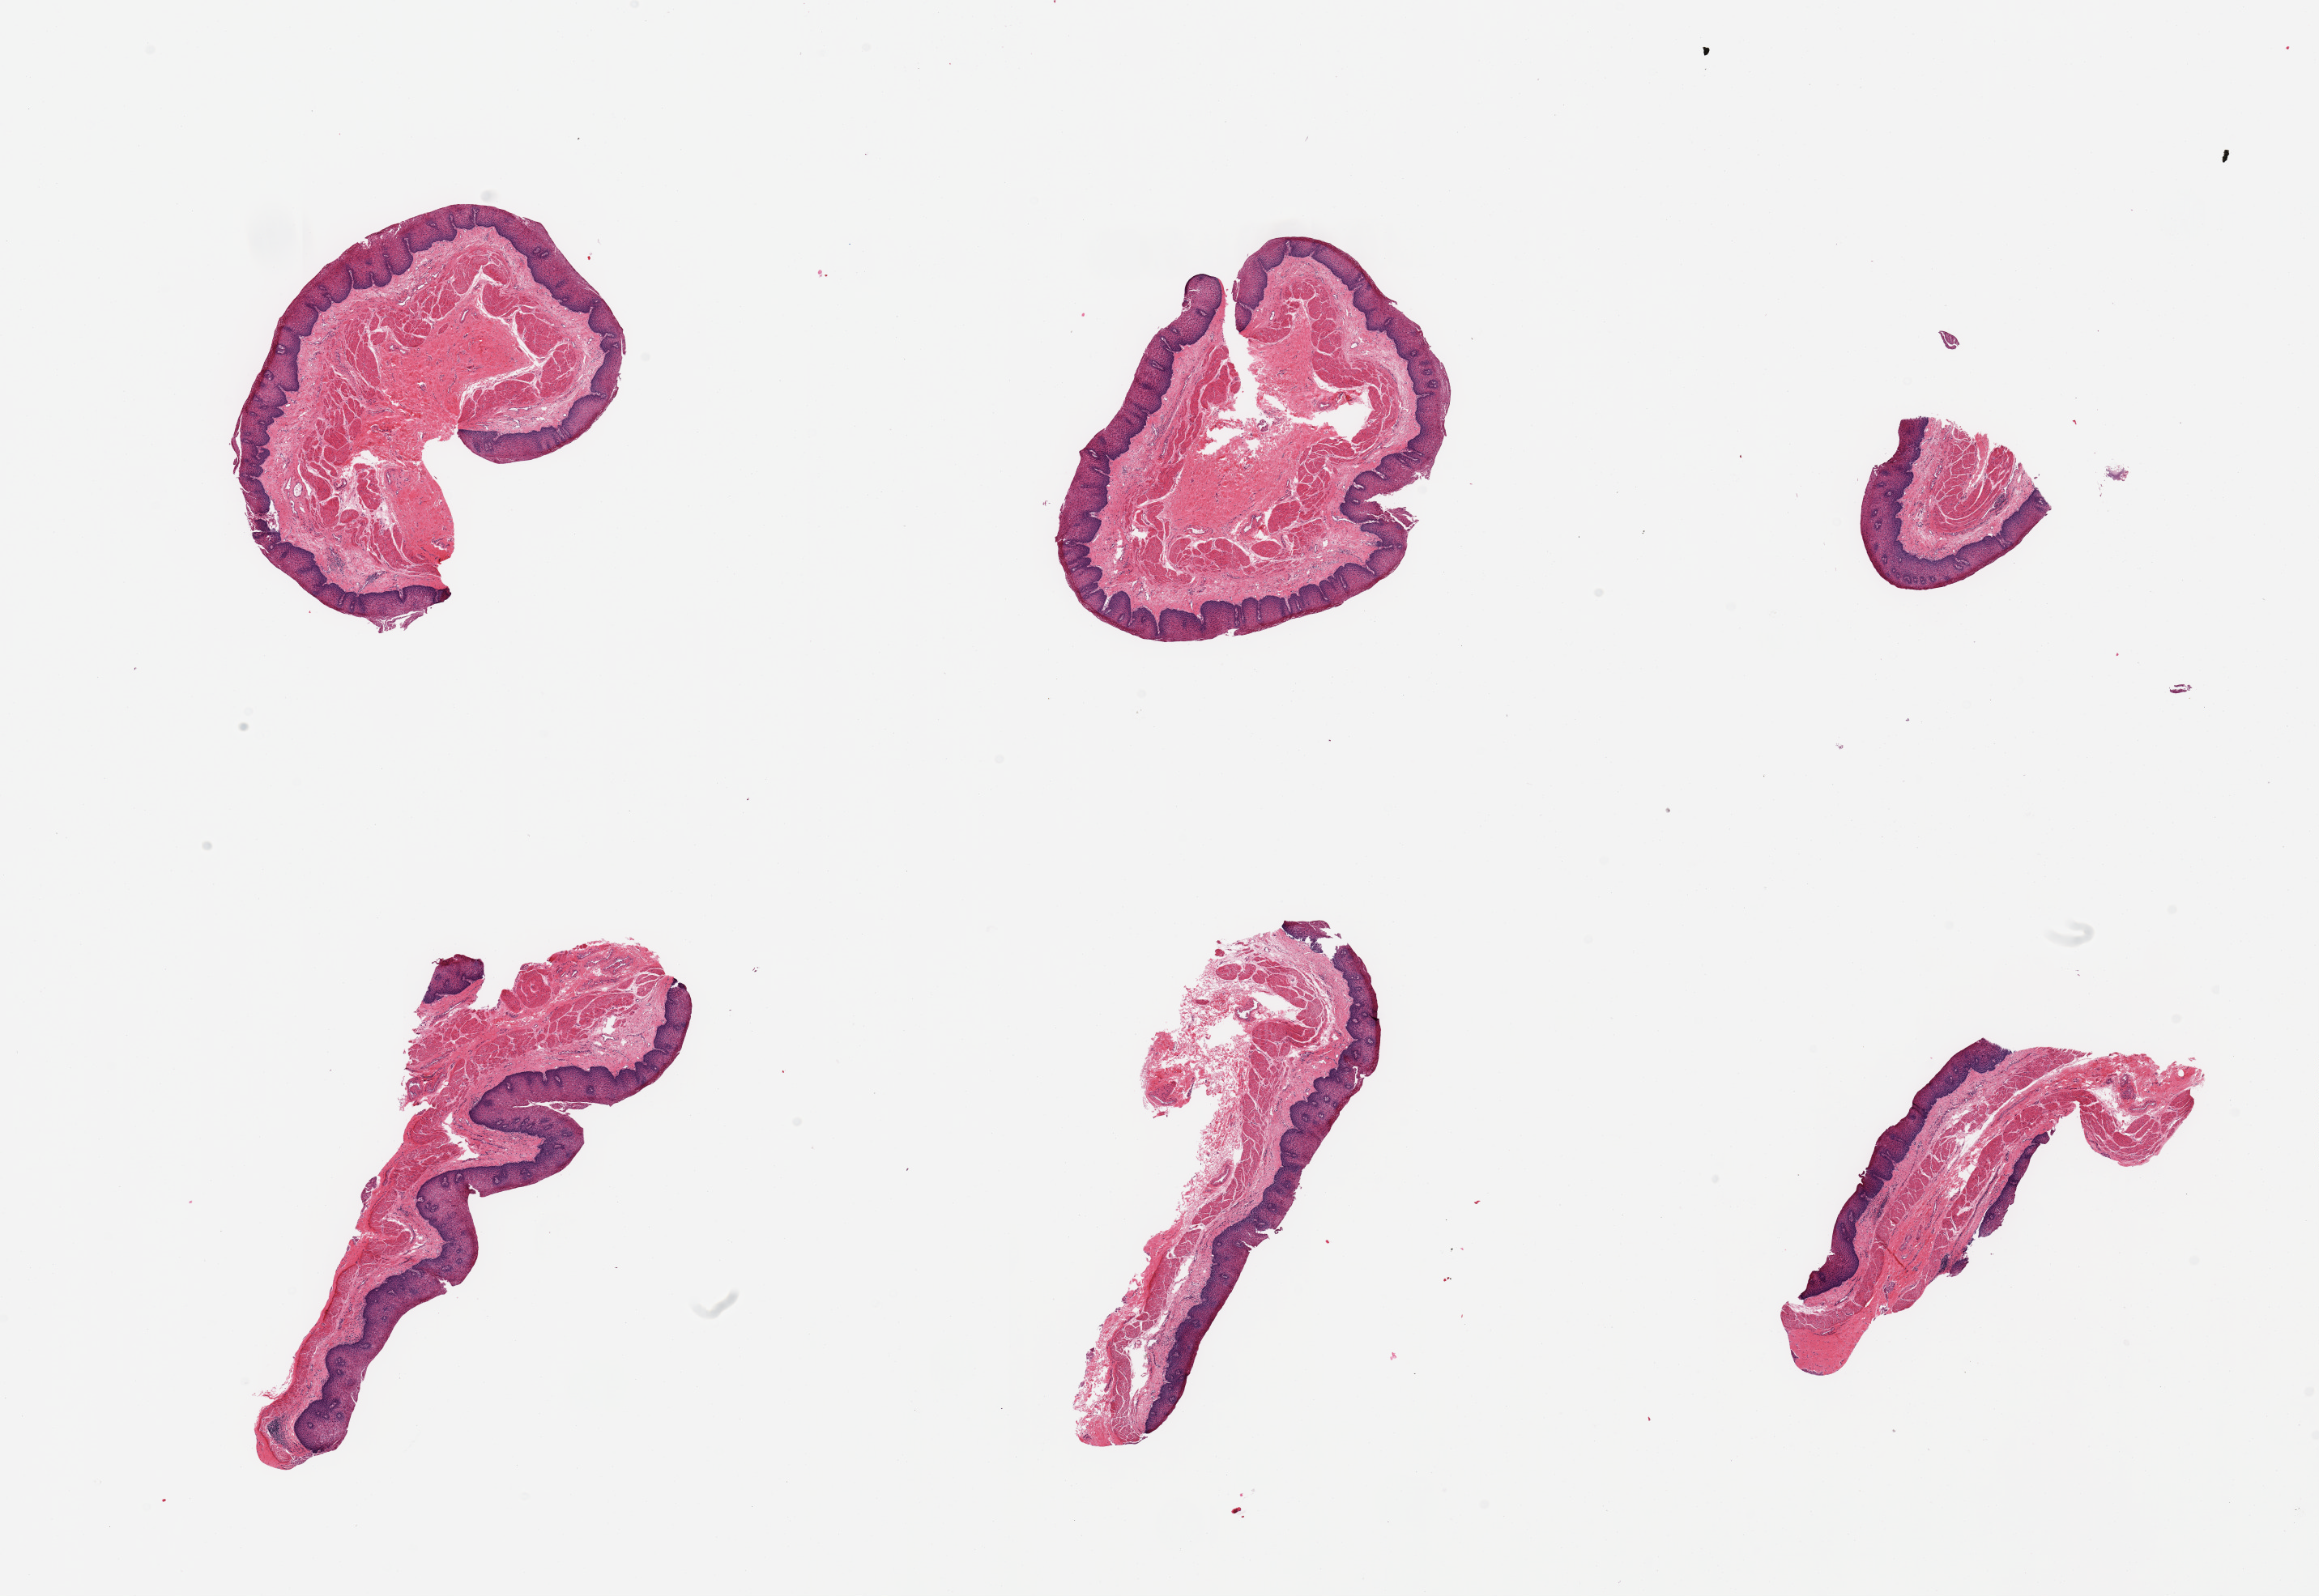
Whole-slide image, haematoxylin and eosin stain, brightfield, shown as a low-resolution overview of the whole scanned area (about 22.6 x 15.6 mm); PAXgene-fixed, paraffin-embedded tissue; section of esophageal mucous membrane (target tissue); tissue donor sample. Male donor.
• review note (as recorded): 6 pieces; mucosa, not muscularis